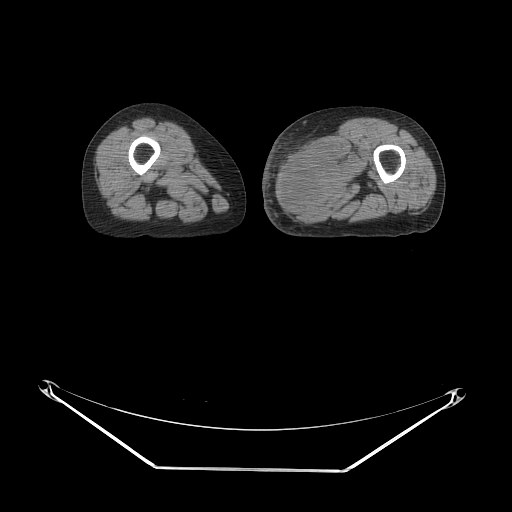
CT of an extremity soft-tissue mass (from a PET/CT study), one axial slice; slice 22 of 91 in the series (ordered by position); 140 kVp; soft-tissue window (W 400 / L 40 HU); 512 × 512 image matrix. Female patient. Case-level facts recorded for this patient, not image findings: histological type: pleomorphic leiomyosarcoma; grade: high; site of the primary tumour: left thigh.
Annotated regions visible in this slice (expert contour drawn on MRI and transferred to this co-registered scan by the dataset authors):
- gross tumour volume including surrounding oedema: bounding box (x1, y1, x2, y2) in pixels: (279, 135, 362, 213)
- gross tumour volume (mass): (279, 149, 352, 213)